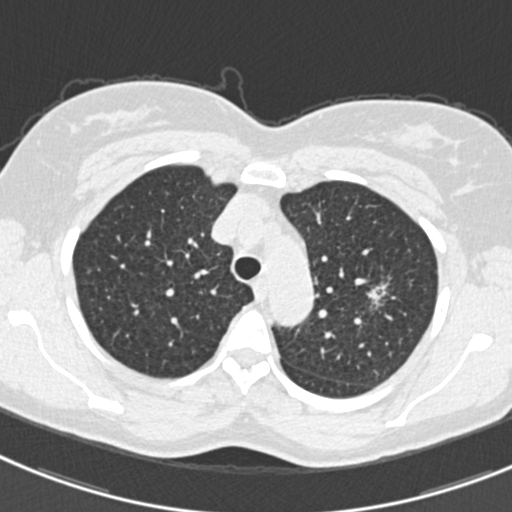
Low-dose screening chest CT, one axial slice; position 242 of 309 along the scan axis; lung window (W 1500 / L -600 HU); 1 mm slice thickness; 512 × 512 image matrix, field of view 302 × 302 mm.
Annotated regions visible in this slice (outlined manually by an expert reader):
- lesion 1 (tumor, upper lobe of left lung): bounding box (x1, y1, x2, y2) in pixels: (369, 284, 386, 304)